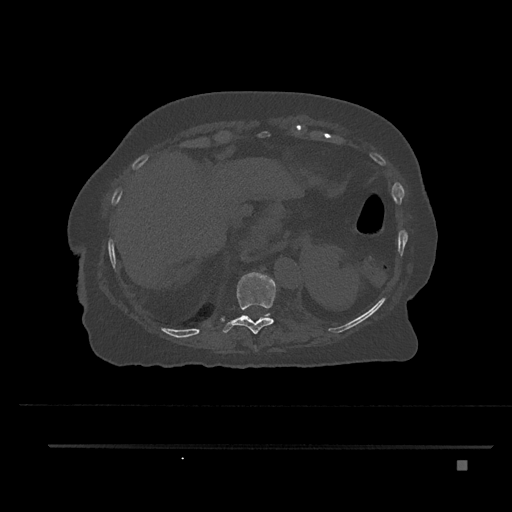
CT including the spine, one axial slice; slice 351 of 797 in the series (ordered by position); reconstruction kernel Br40s/3; 120 kVp; bone window (W 1800 / L 400 HU); 512 × 512 image matrix, field of view 437 × 437 mm. Female patient, age 76 years. From the clinical record (not read from this slice): primary cancer: lung.
Annotated regions visible in this slice (semi-automatic segmentation, software-assisted and operator-edited):
- T10 vertebra: bounding box (x1, y1, x2, y2) in pixels: (221, 272, 276, 334)
- T11 vertebra: (245, 314, 270, 316)
- T9 vertebra: (254, 346, 256, 350)